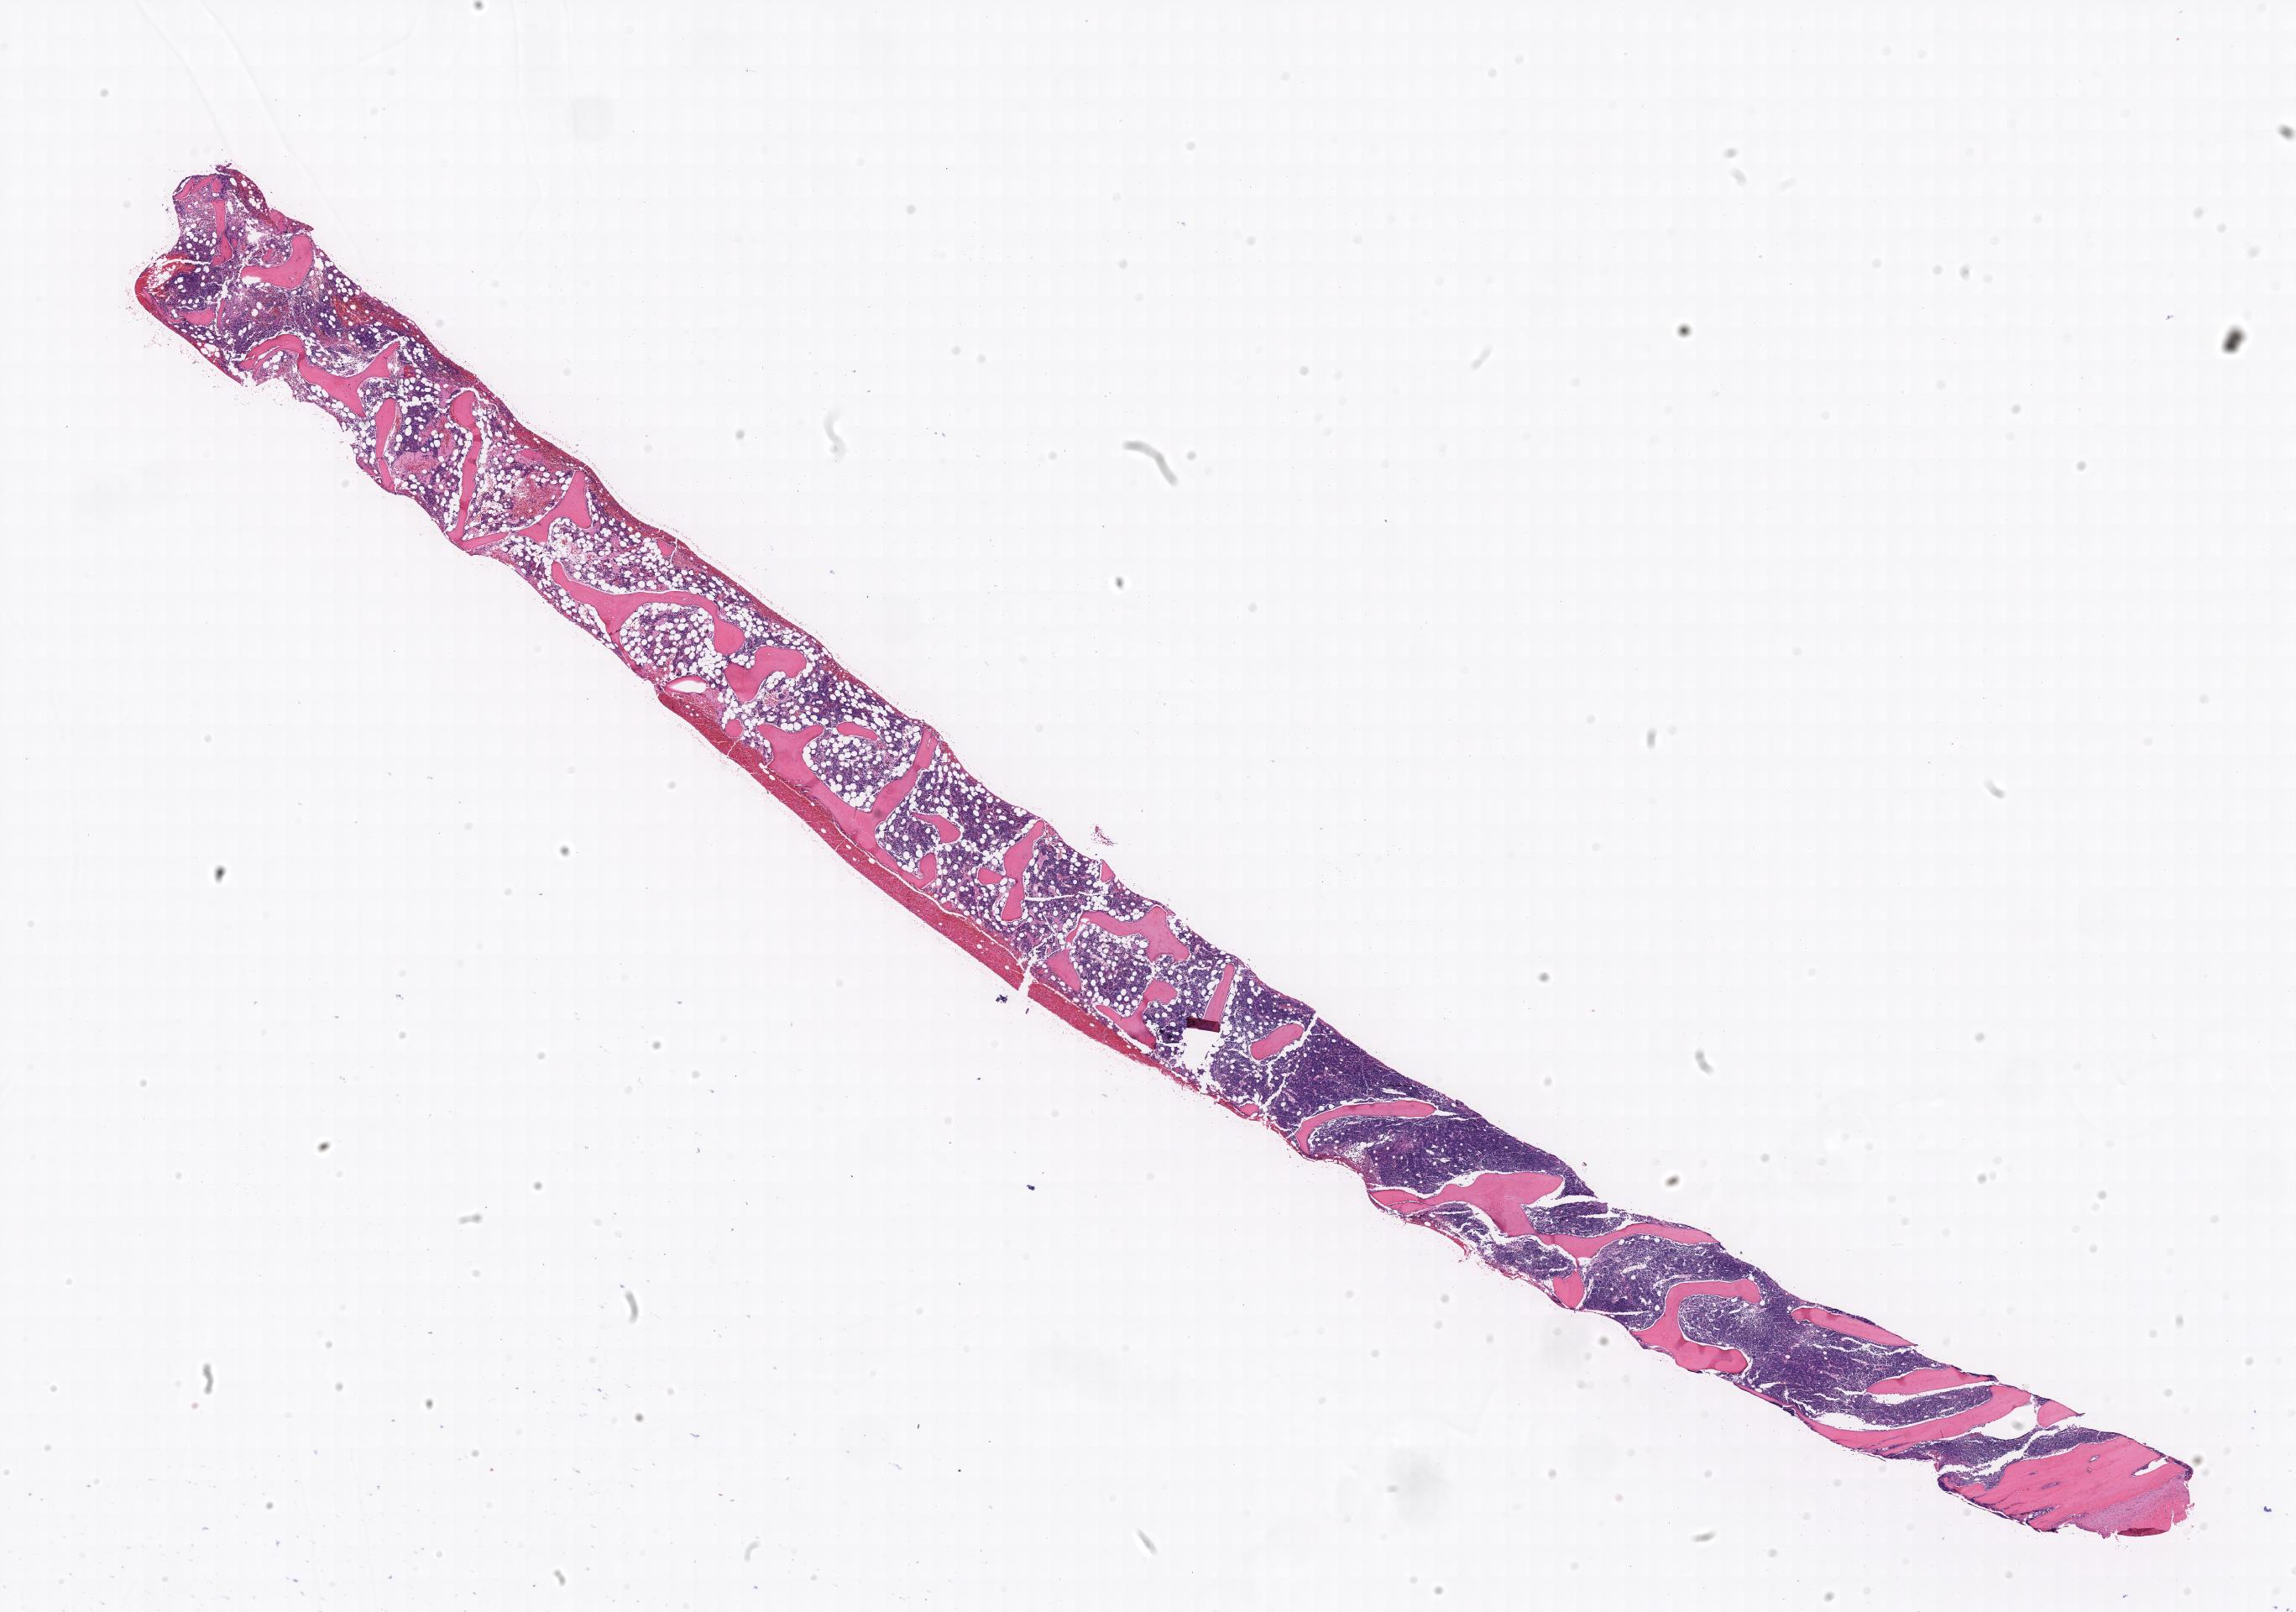
Whole-slide image, haematoxylin and eosin stain, a low-resolution overview of the entire scanned area. Tumor tissue. Patient male; age 12 years.
Histologic diagnosis: Burkitt lymphoma, NOS.